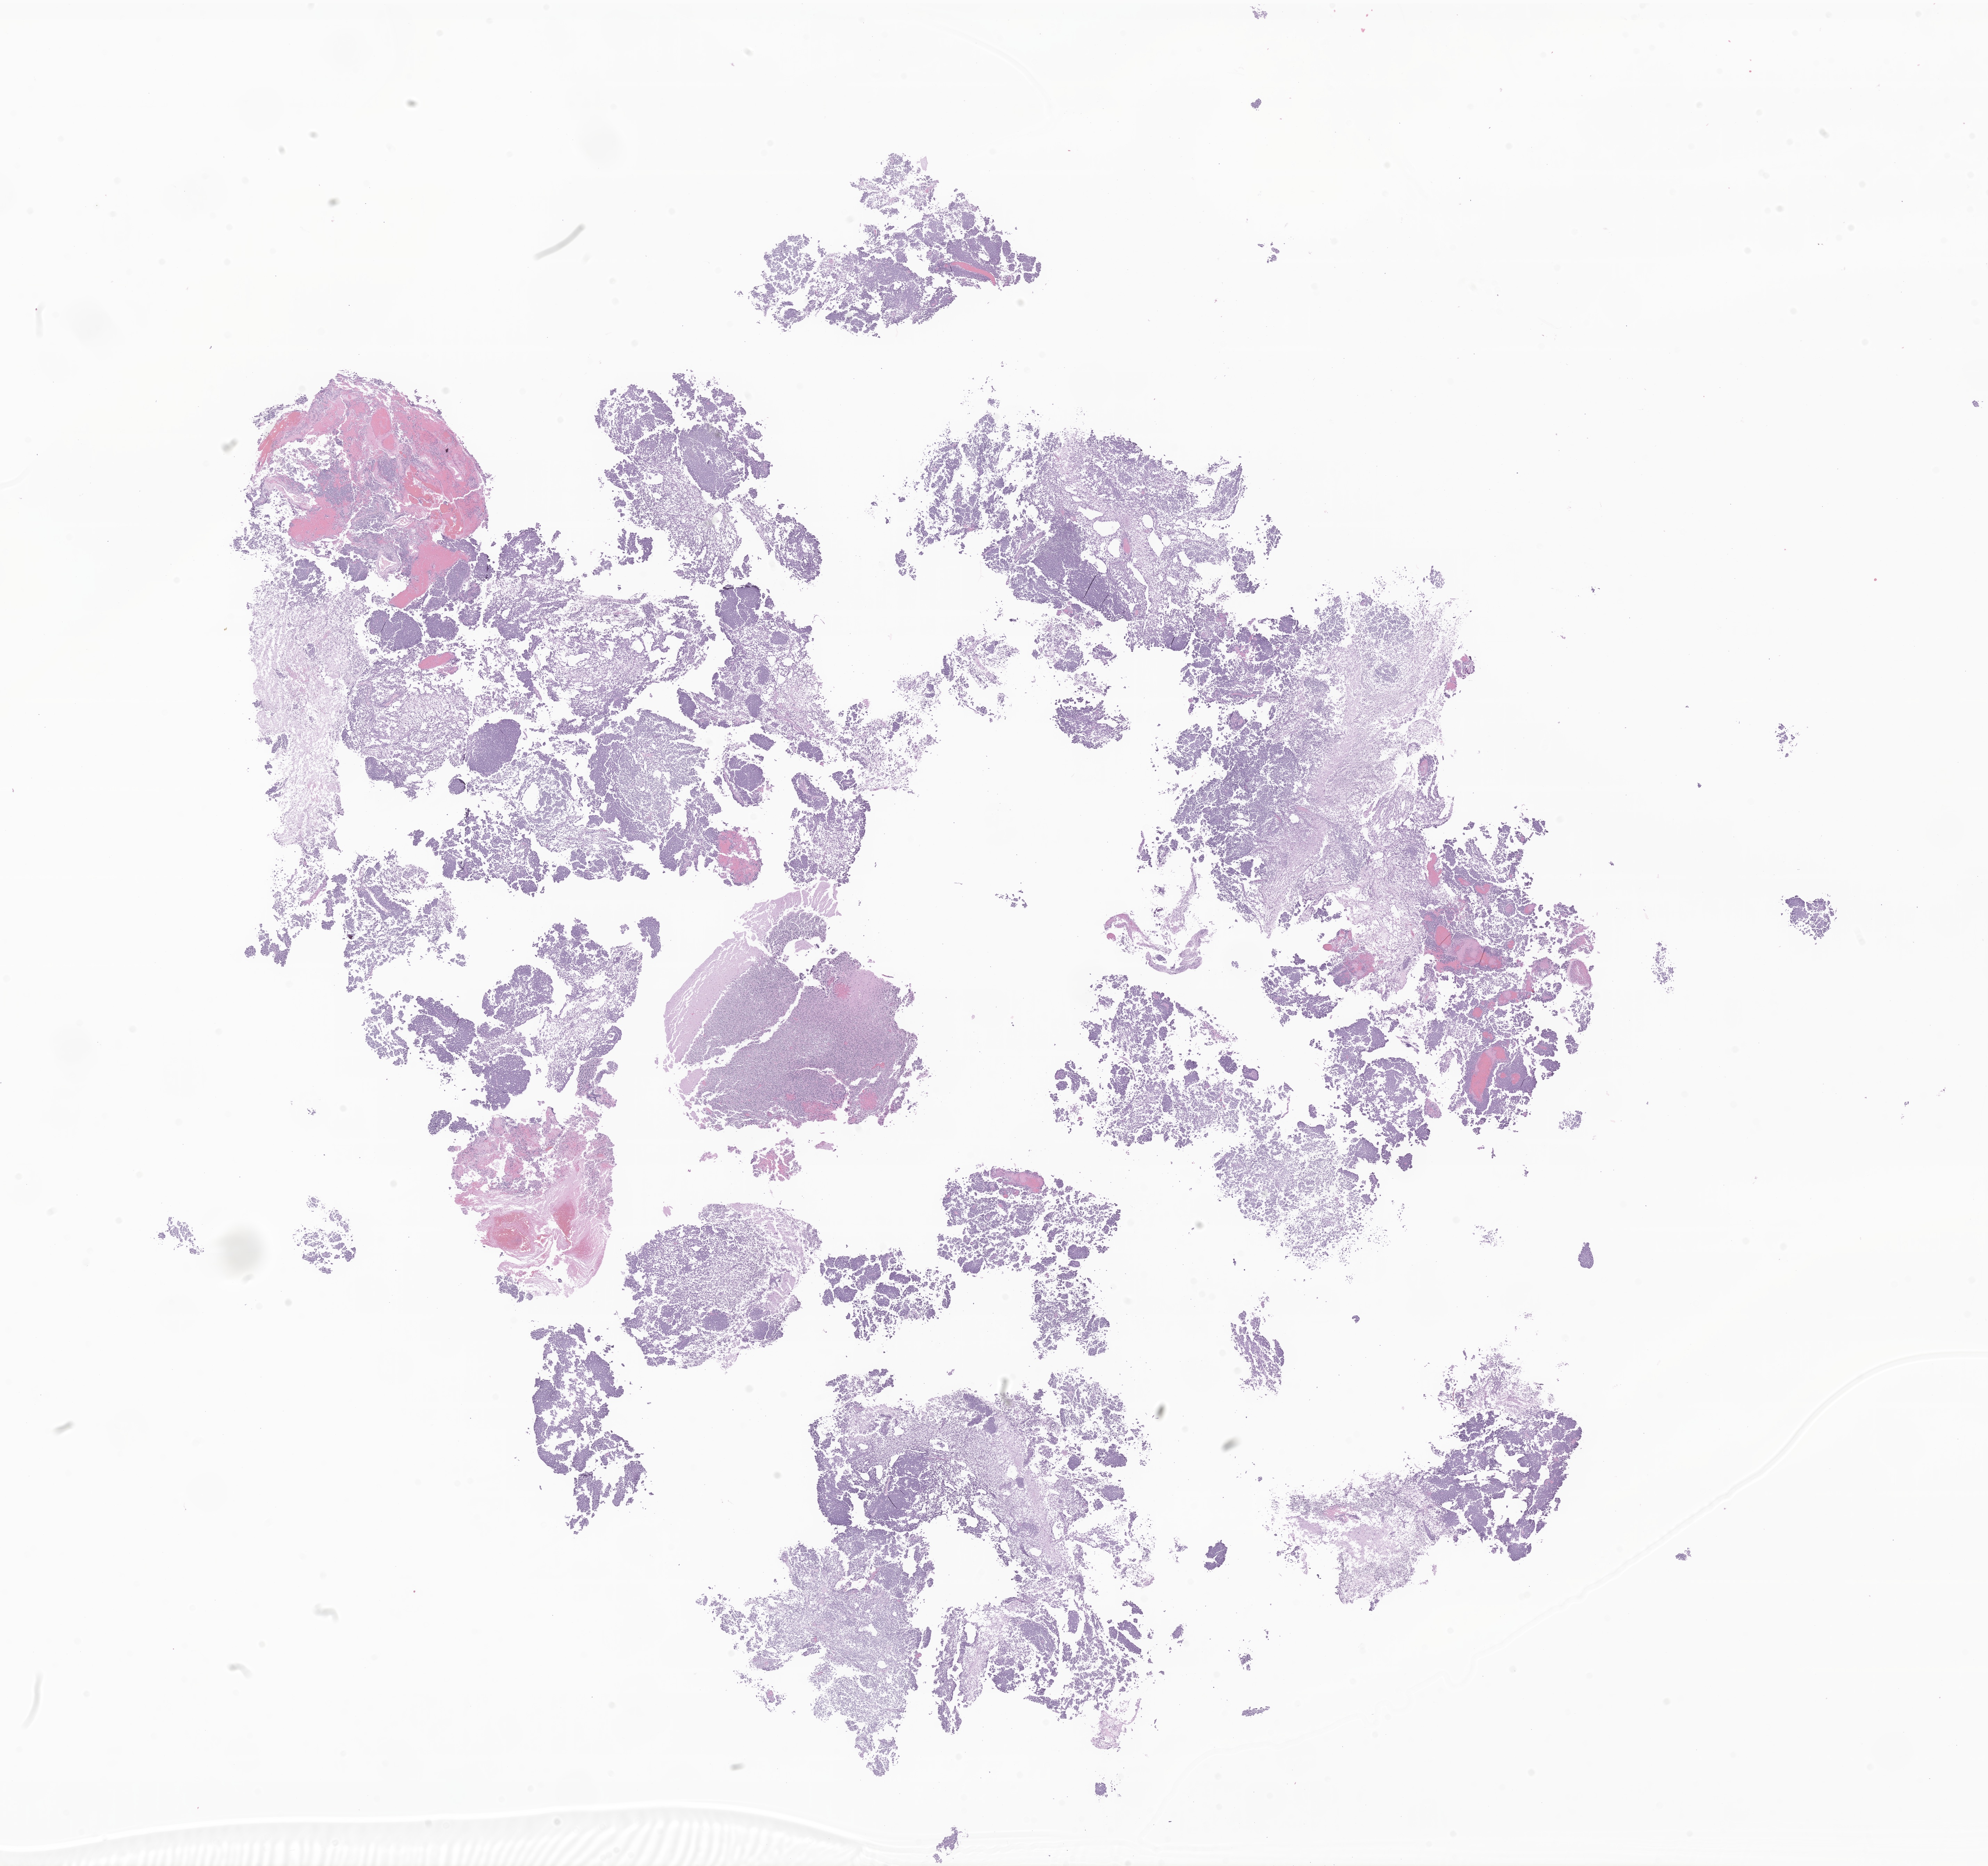
Haematoxylin and eosin whole-slide image of tumor tissue from the brain, a low-resolution overview of the entire scanned area, about 24.1 x 22.6 mm; formalin-fixed paraffin-embedded section. Patient male; age 288 months.
* recorded diagnosis: Medulloblastoma, NOS